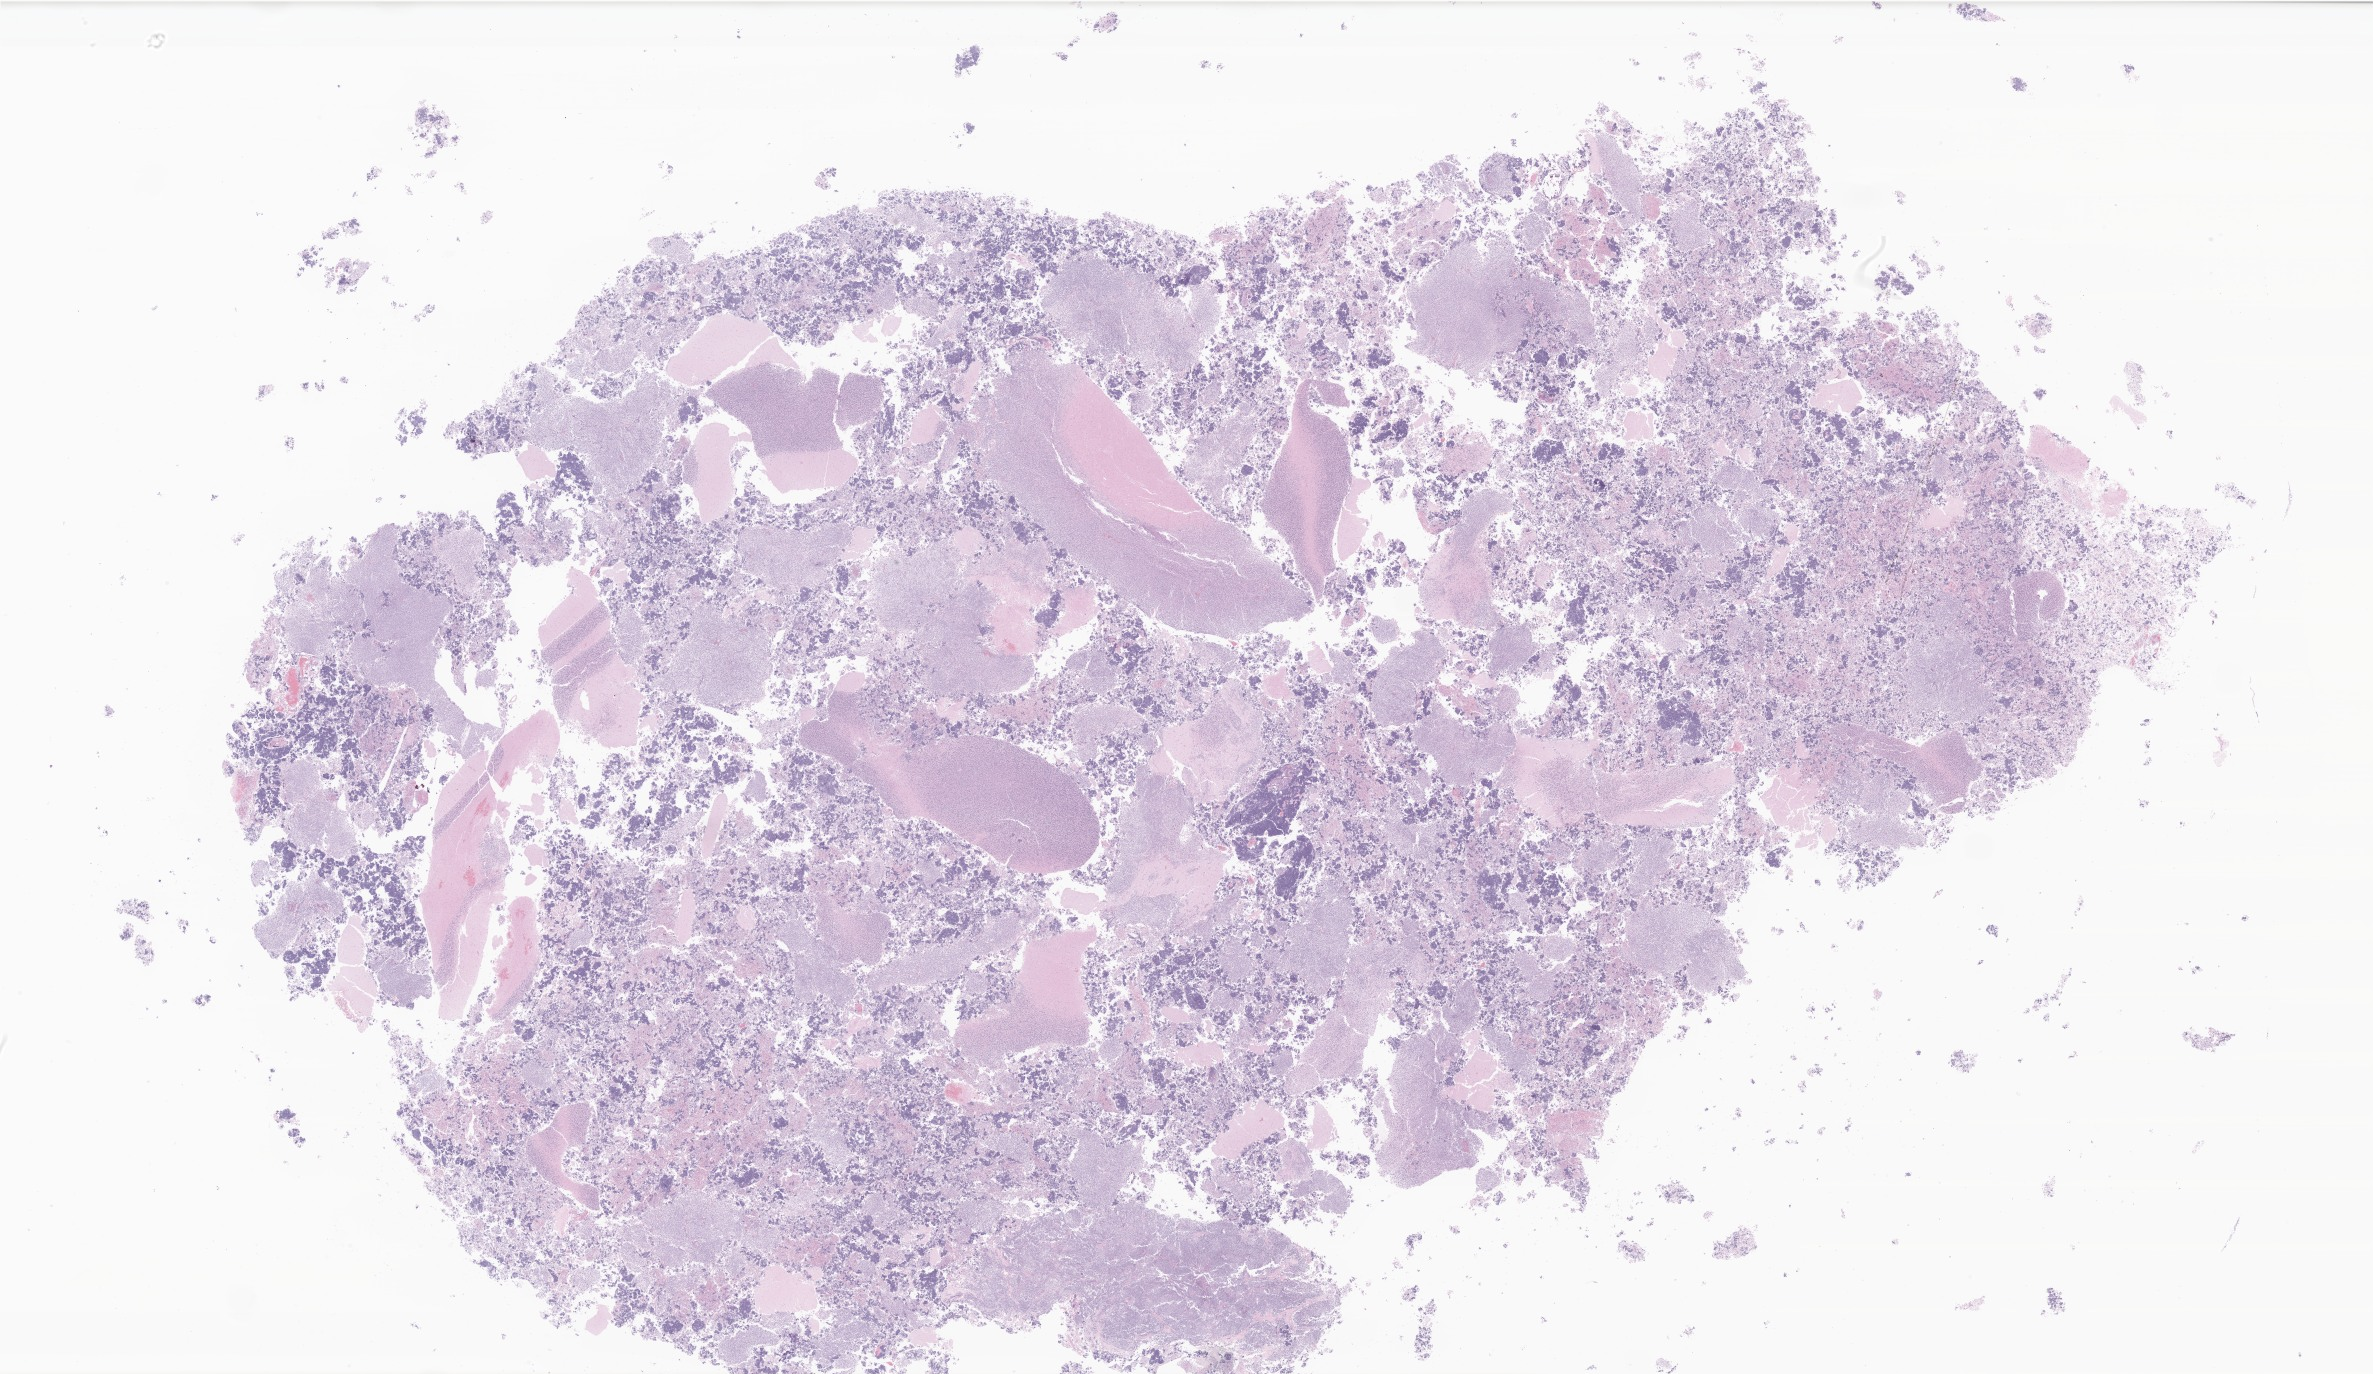
Whole-slide image, hematoxylin and eosin (H&E) stain of tumor tissue from the cerebellum, whole scanned area (about 40.0 x 23.2 mm) shown as a low-resolution overview. Formalin-fixed, paraffin-embedded (FFPE) tissue. Male patient, age 149 months (12 years 5 months).
Diagnosis: Medulloblastoma, NOS.